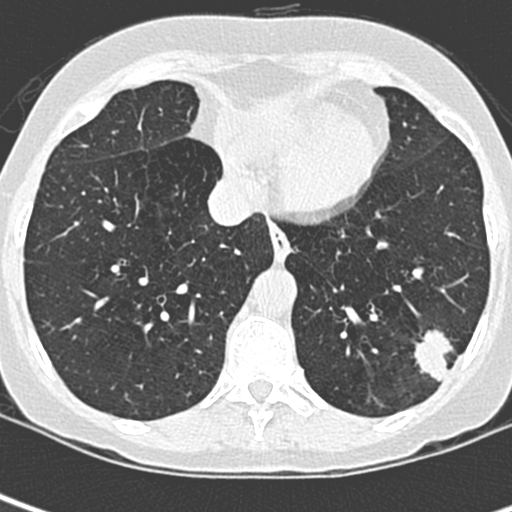
Low-dose screening chest CT, one axial slice; position 88 of 252 along the scan axis; 120 kVp; lung window (W 1500 / L -600 HU); 1.3 mm slice thickness; 512 × 512 image matrix, field of view 271 × 271 mm.
Outlined on this slice (expert manual segmentation):
- lesion 1 (tumor, lower lobe of left lung): box from (x=414, y=329) to (x=454, y=381) px